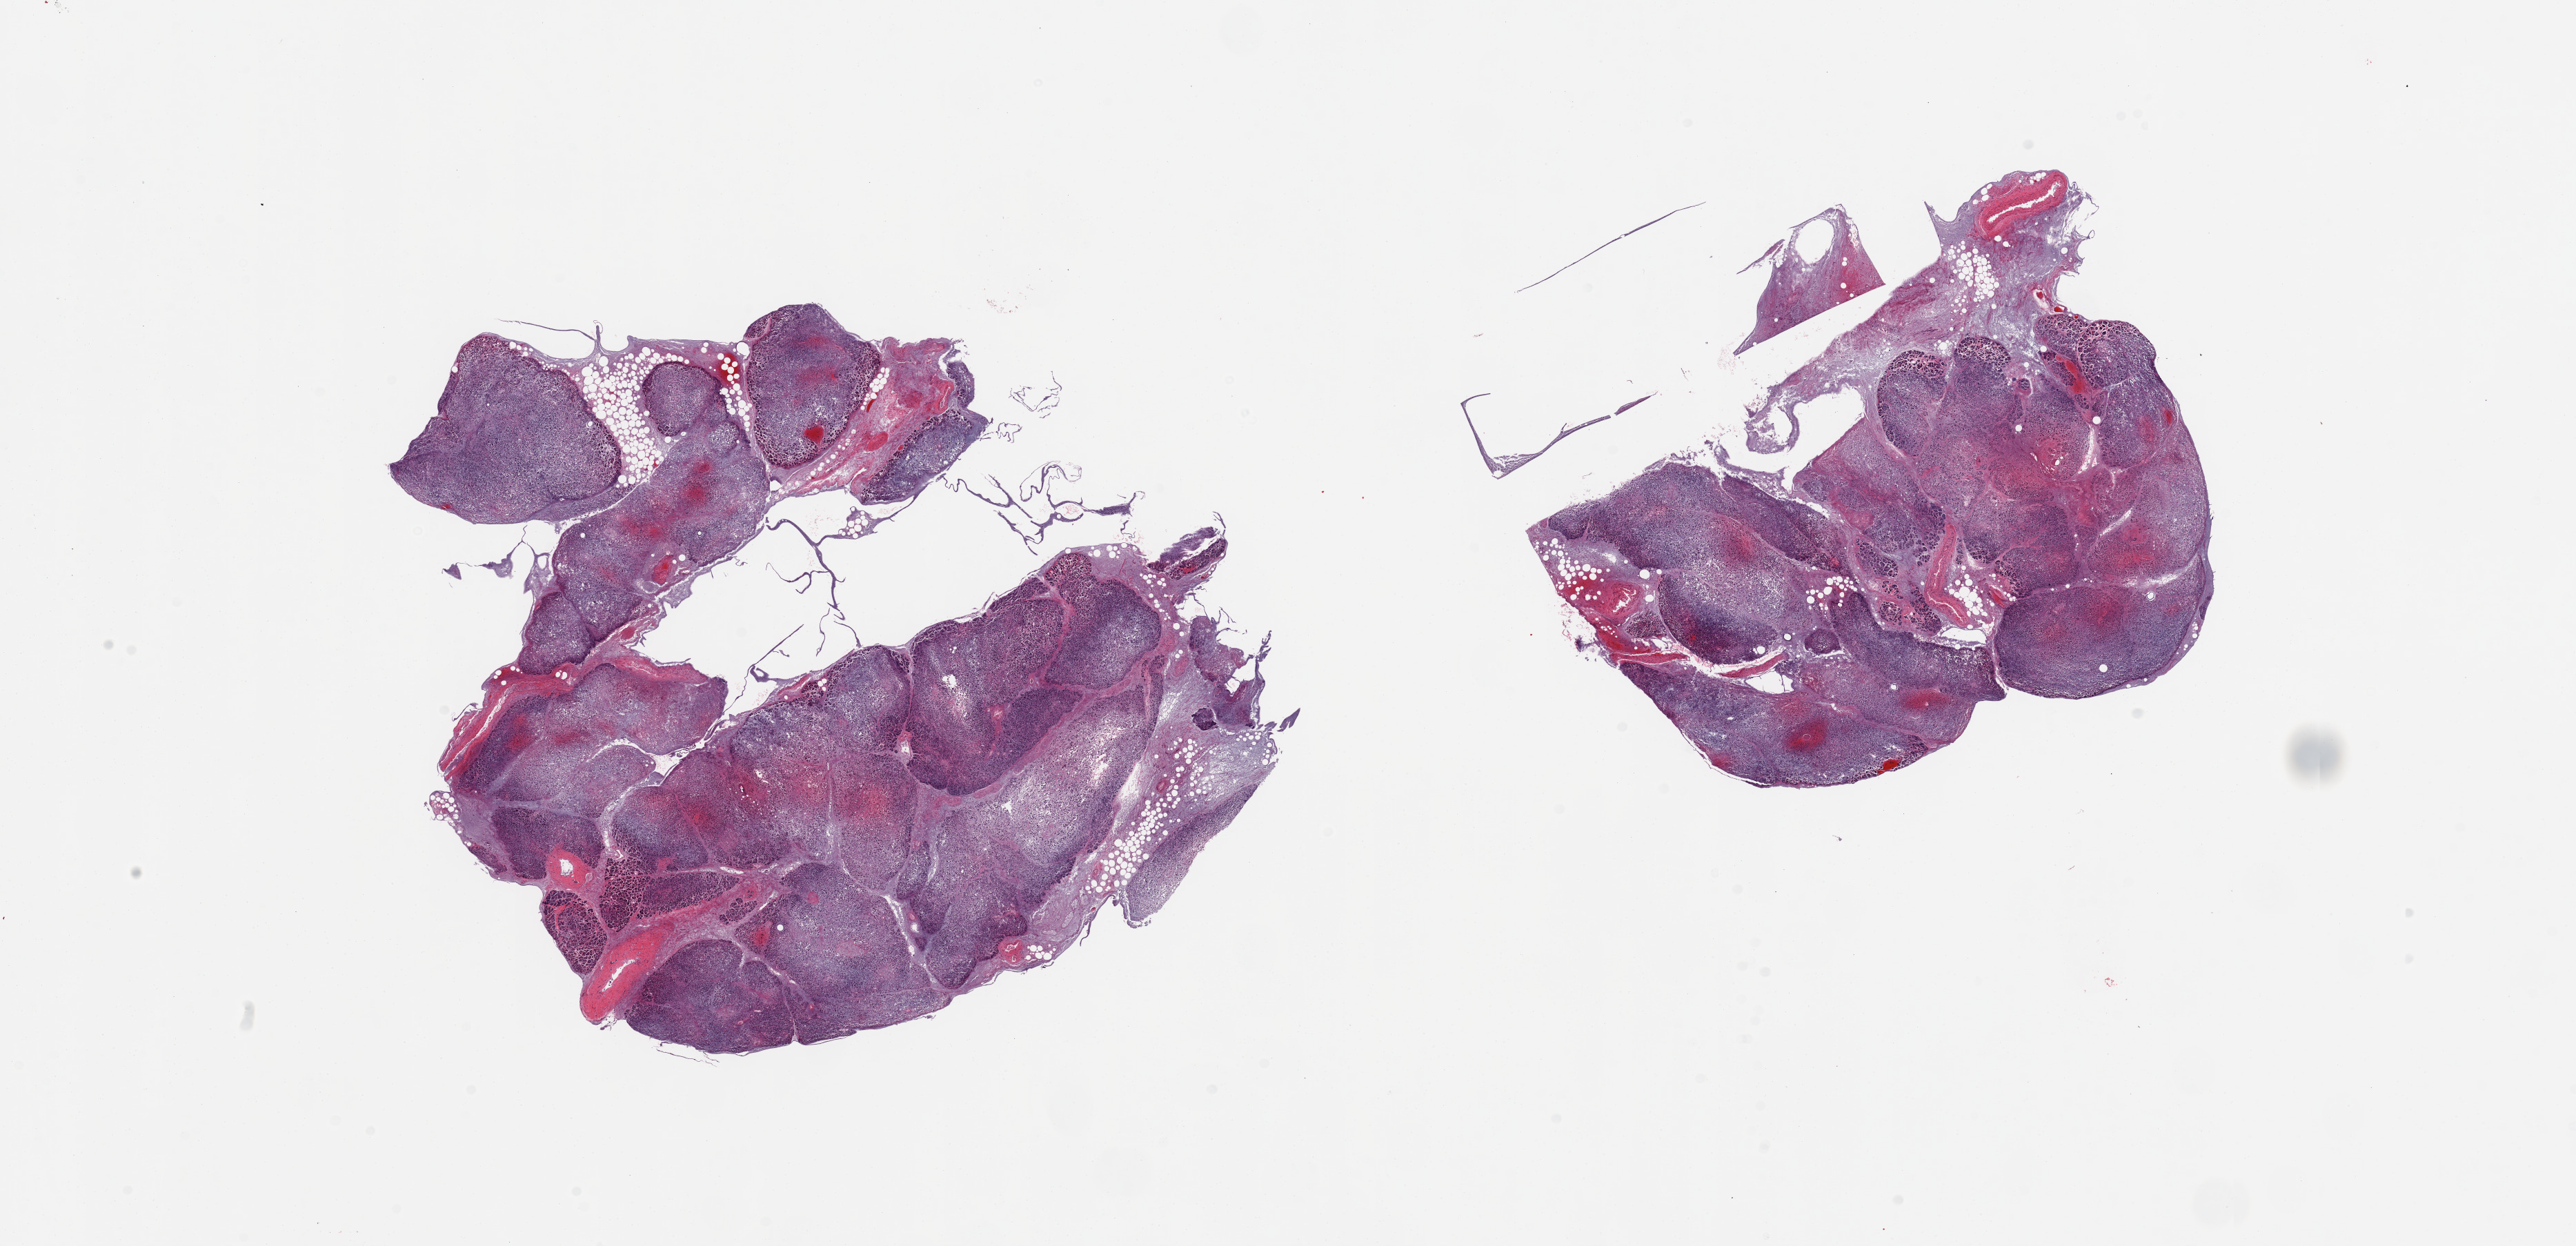
Haematoxylin and eosin whole-slide image, low-resolution overview of the scanned area, about 29.5 x 14.3 mm; PAXgene-fixed paraffin-embedded (PFPE) section; sampled site (target tissue): pancreas; donor tissue sample. Male donor.
Pathologist's review note for this sample: 2 pieces, marked autolysis/saponfication; Islets not well preserved.